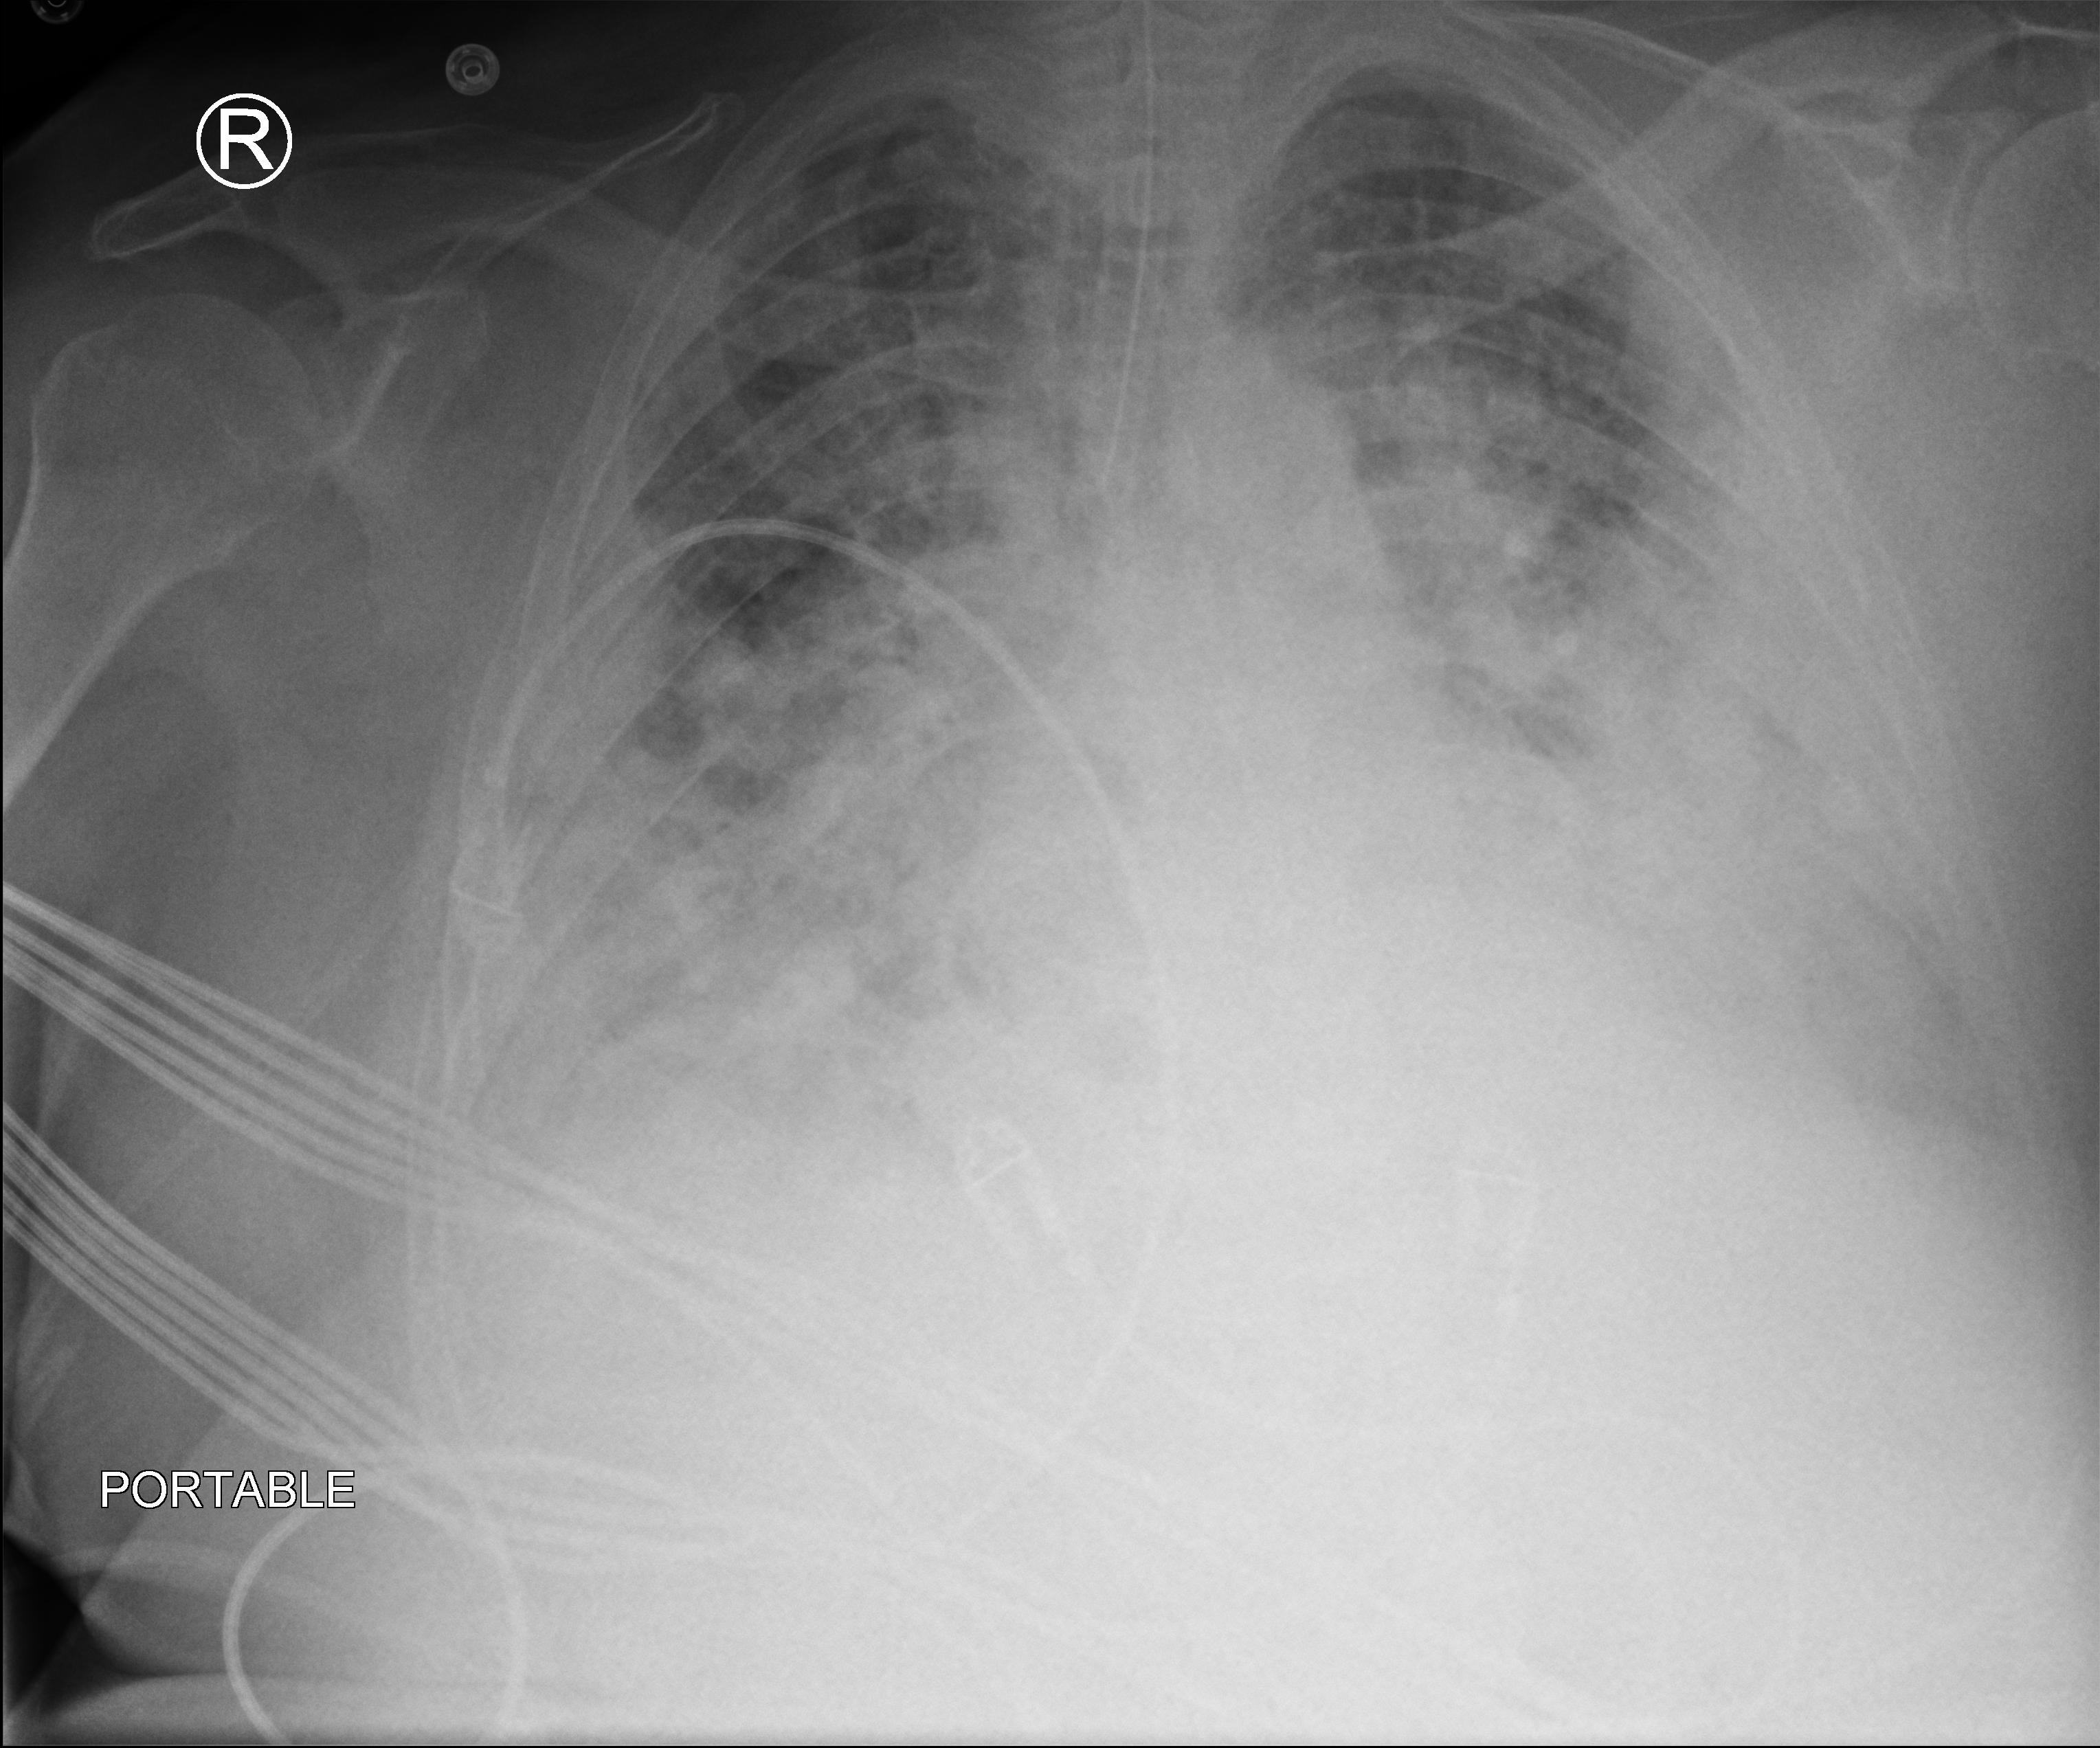
Portable chest radiograph, anteroposterior (AP) projection. Male patient hospitalised with COVID-19, age 60–74 years.
Hospital-stay facts (about this admission, not read from this image; timing relative to this image not recorded):
- diabetes (admission record): yes
- mechanically ventilated during this hospital stay: yes